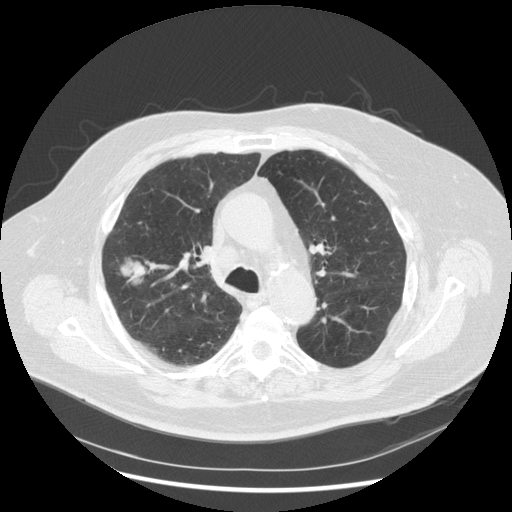
Low-dose screening chest CT, one axial slice. Position 189 of 263 along the scan axis. Reconstruction kernel STANDARD. Lung window (W 1500 / L -600 HU). 2.5 mm slice thickness. 512 × 512 image matrix, field of view 400 × 400 mm.
Outlined on this slice (outlined manually by an expert reader):
- lesion 1 (tumor, upper lobe of right lung): bounding box <120,258,146,286> (left, top, right, bottom; pixels)